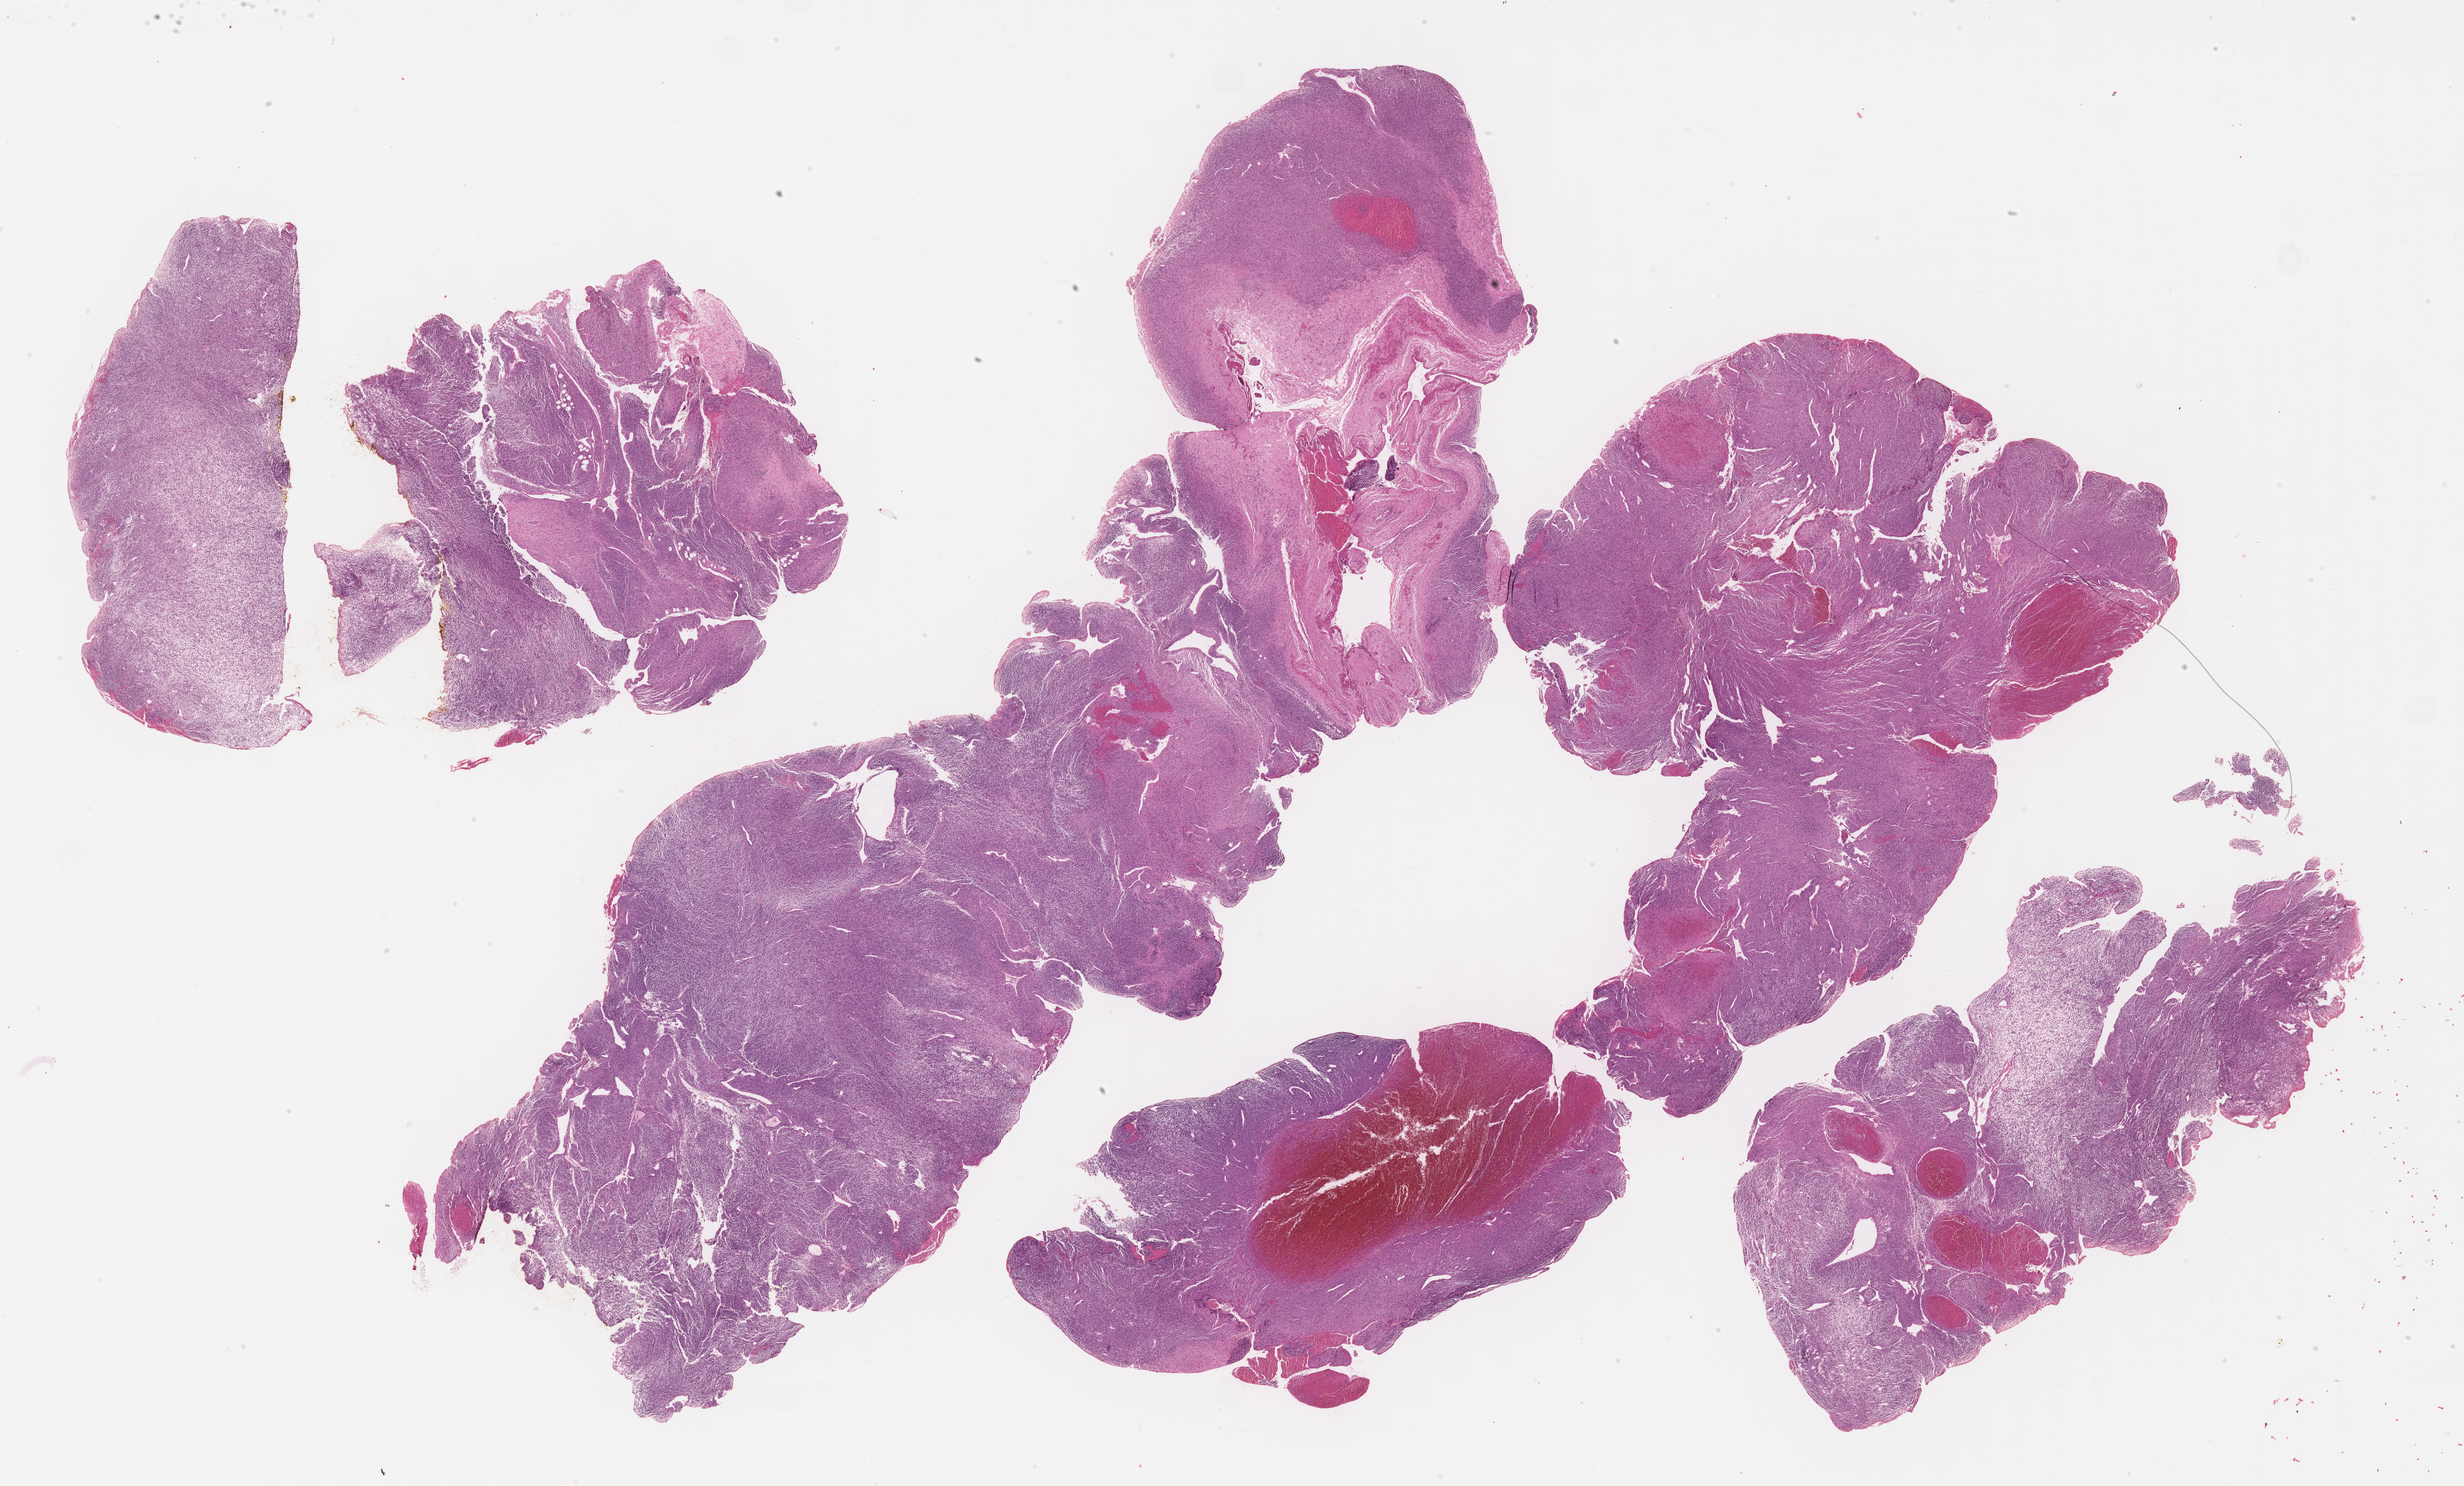
Hematoxylin and eosin (H&E) whole-slide image of tumor tissue, a low-resolution overview of the entire scanned area, about 31.2 x 18.8 mm. FFPE section. Site: pelvis. Patient: male, age 1.0 years at diagnosis.
• metastatic status at presentation (as recorded): non-metastatic
• diagnosis: rhabdomyosarcoma; histological classification: embryonal rhabdomyosarcoma
• stage (as recorded): 3